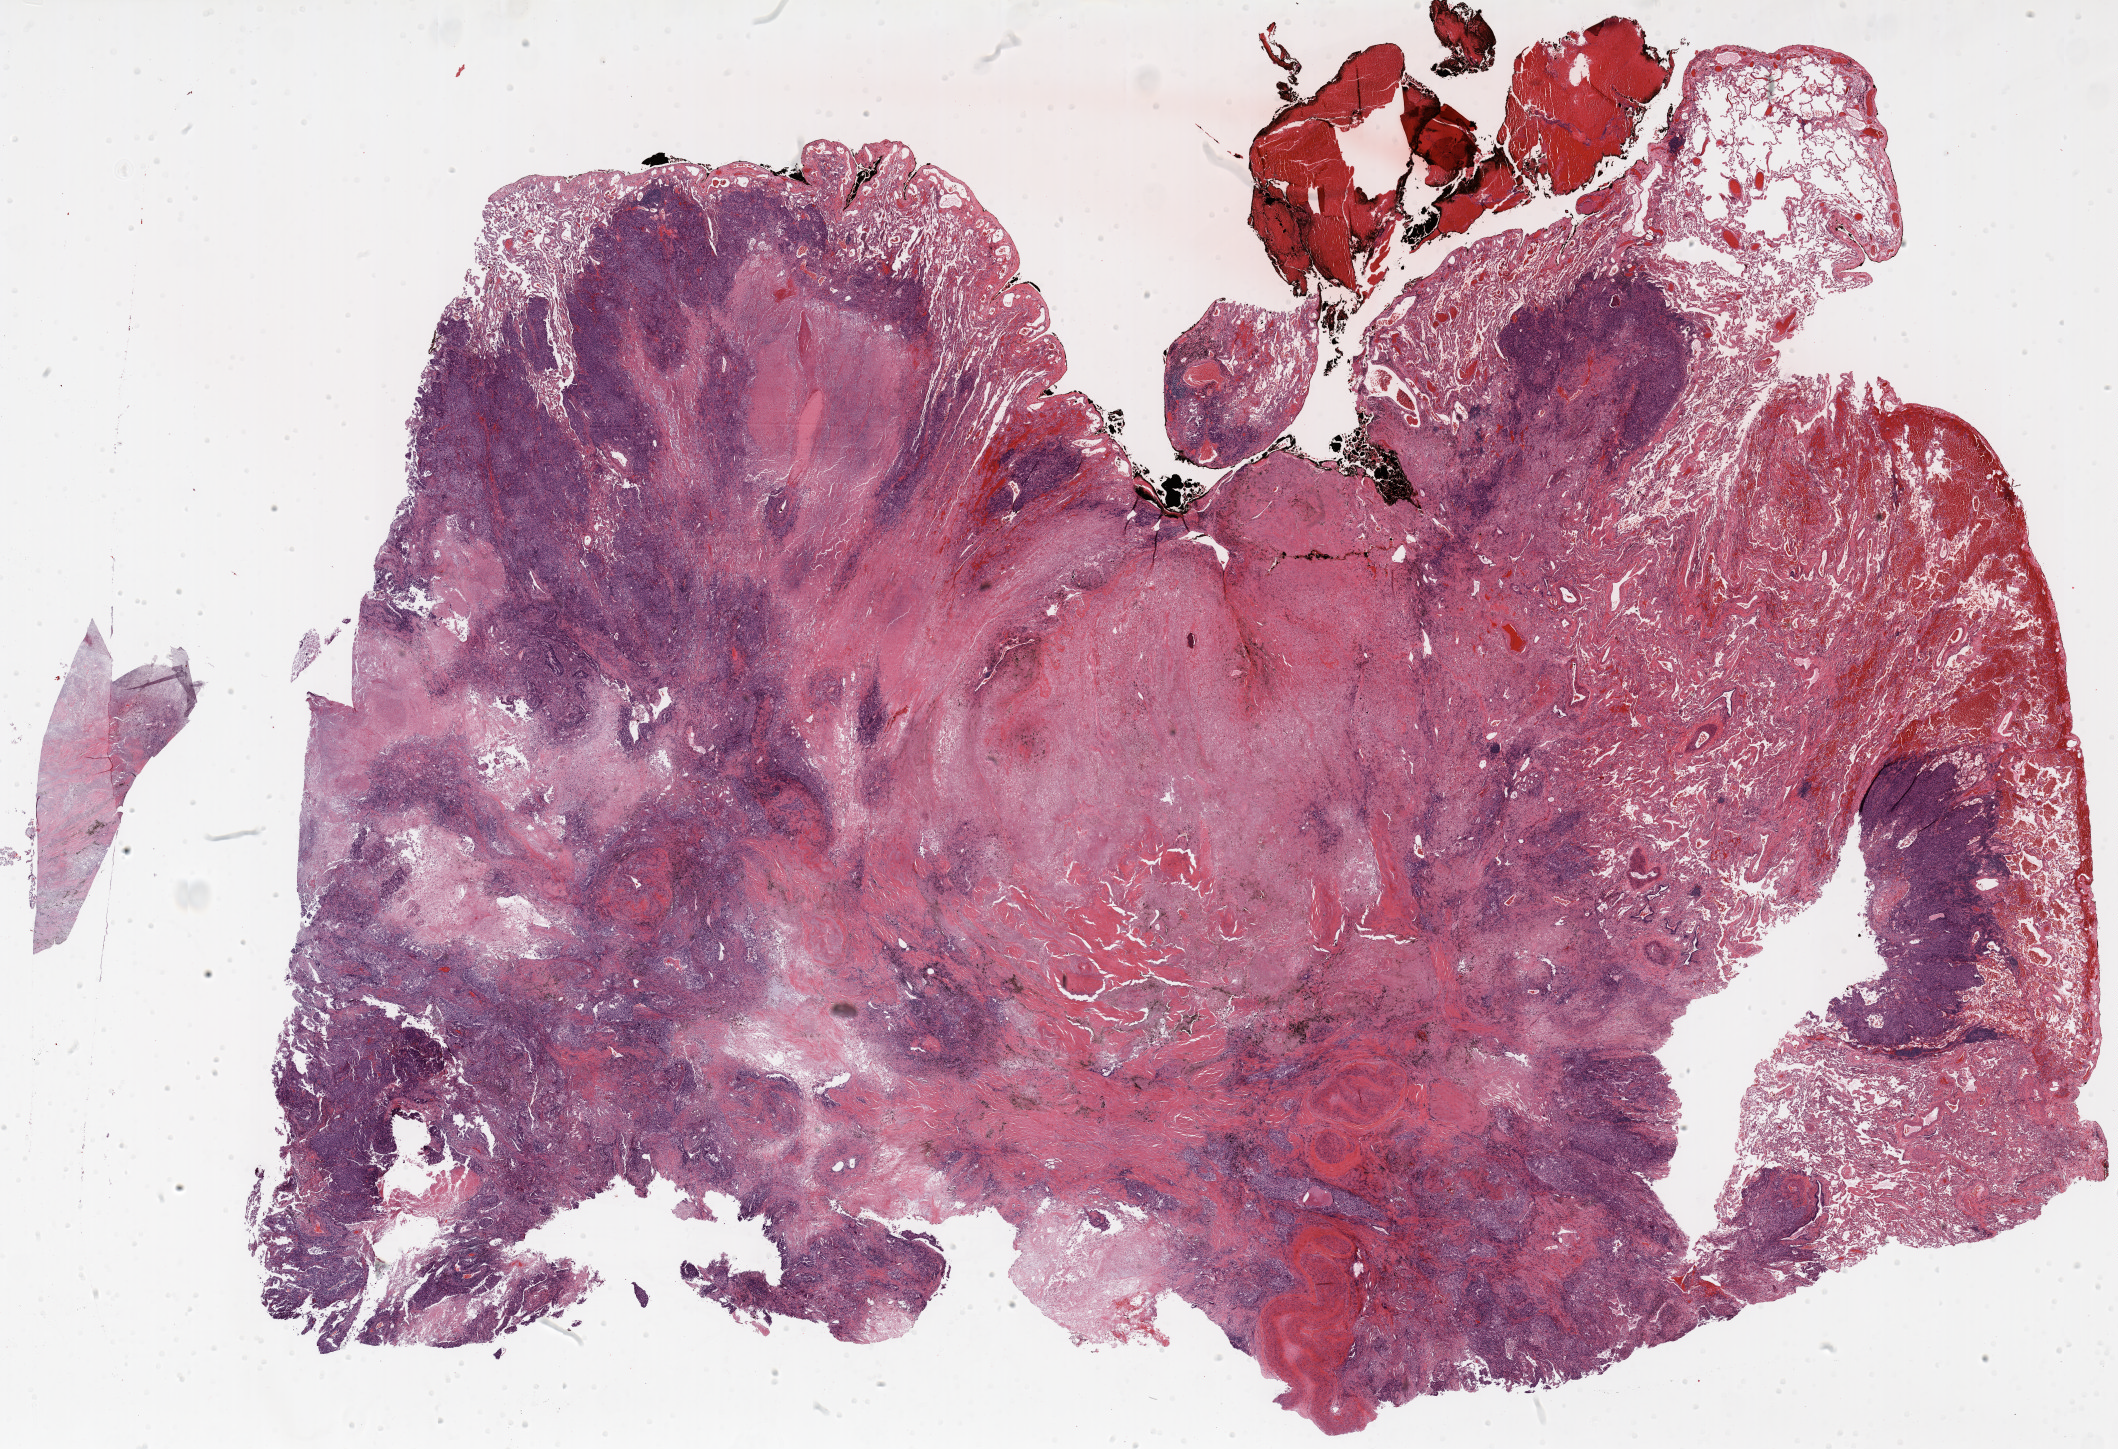
Whole-slide histology image, H&E-stained, low-resolution overview of the scanned area, about 34.0 x 23.3 mm (acquisition: 20x scan); FFPE section; lung tissue. Male patient, aged 69 at enrolment. Current smoker at enrolment. Grade: poorly differentiated (G3).
Primary tumour location (clinical record): right upper lobe. Stage (AJCC 6th edition): IB. Participant's lung-cancer diagnosis: Adenocarcinoma, NOS. Tumour size (pathology): 40 mm.